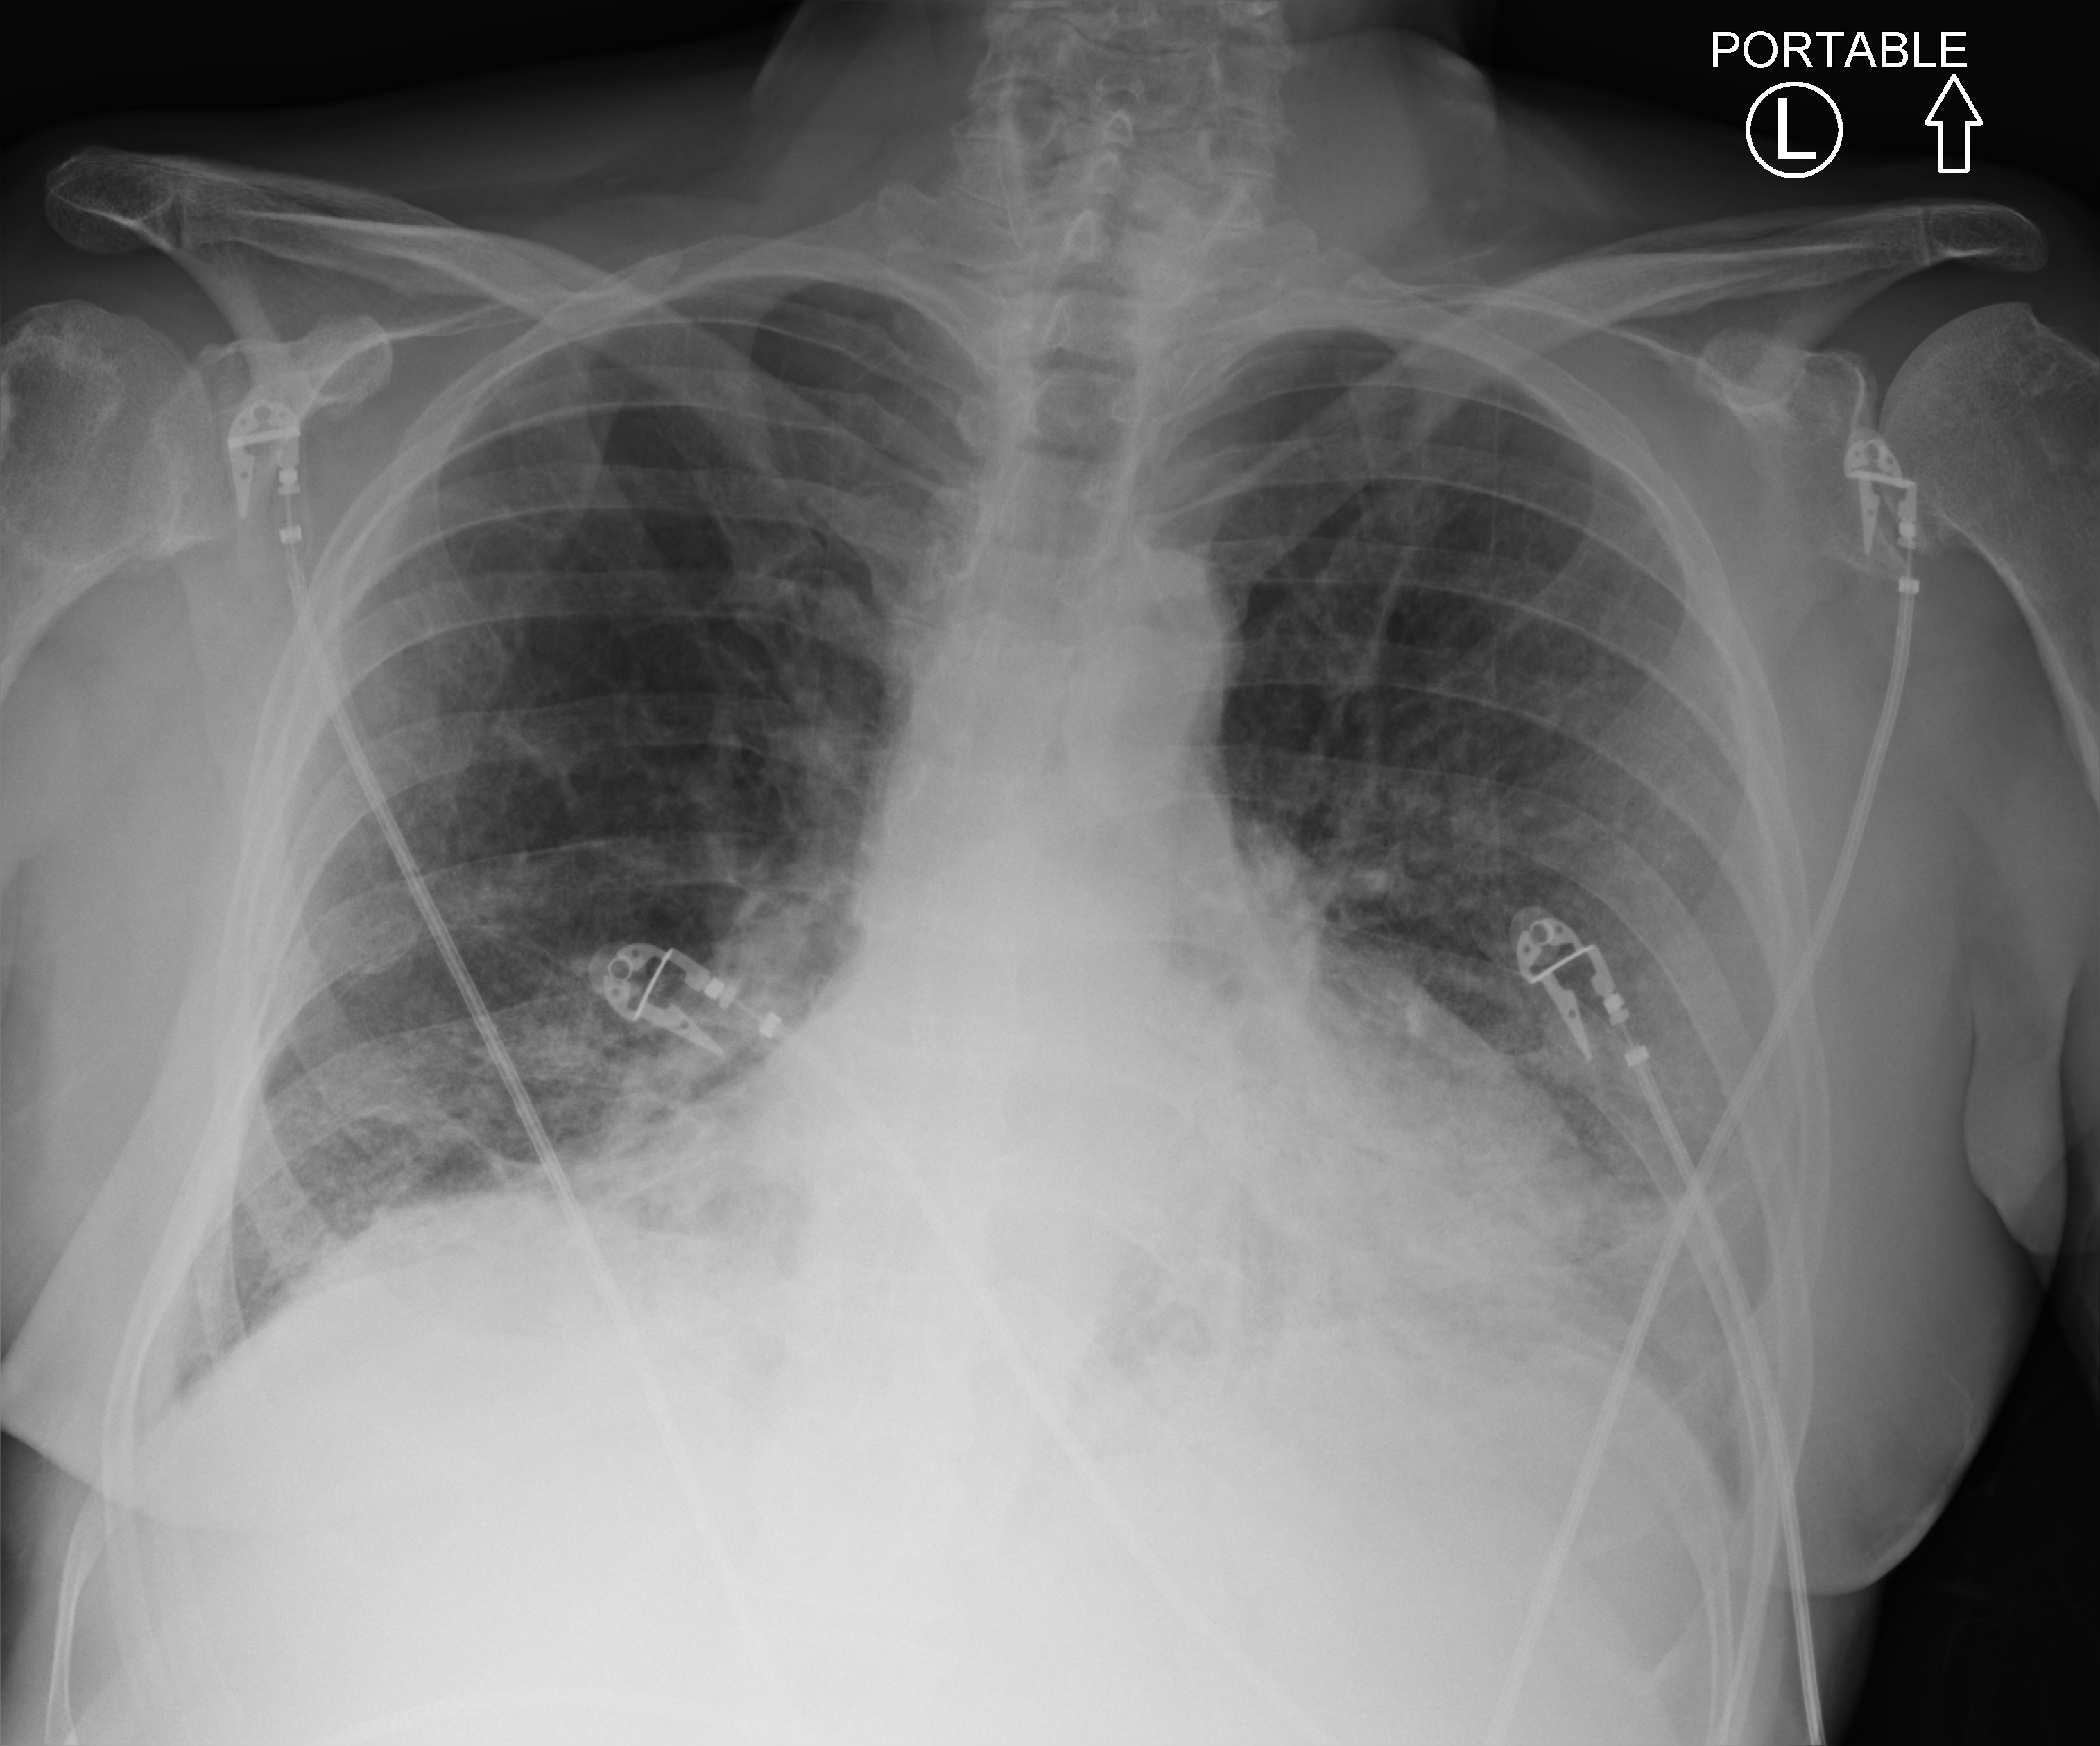
Chest X-ray (portable); anteroposterior (AP) projection. Male patient hospitalised with COVID-19, age 60–74 years.
Hospital-stay facts (about this admission, not read from this image; timing relative to this image not recorded):
- admitted to intensive care during this hospital stay: no
- mechanically ventilated during this hospital stay: no